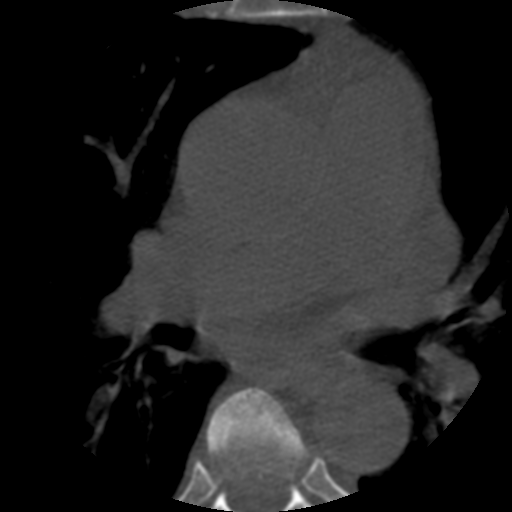
CT including the spine, one axial slice. Position 365 of 508 along the scan axis. 120 kVp. Bone window (W 1800 / L 400 HU). 512 × 512 image matrix. Patient age 57 years. Case-level facts recorded for this patient, not image findings: primary cancer: prostate.
Annotated regions visible in this slice (semi-automatically segmented with operator editing):
- T5 vertebra: bounding box [x1, y1, x2, y2] px = [207, 387, 306, 479]
- T6 vertebra: [211, 463, 311, 512]